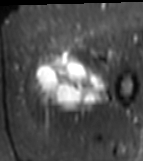
MRI of an extremity soft-tissue mass, one axial slice; position 19 of 81 along the scan axis; STIR; MR volume resampled by the dataset authors to the PET/CT grid (not the native acquisition matrix); 143 × 161 image matrix. Female patient. Case-level facts recorded for this patient, not image findings: histological type: myxofibrosarcoma; grade: intermediate; site of the primary tumour: left thigh.
Outlined on this slice (expert contour drawn on MRI and transferred to this co-registered scan by the dataset authors):
- gross tumour volume including surrounding oedema: bounding box <31,47,109,112> (left, top, right, bottom; pixels)
- gross tumour volume (mass): <33,49,107,112>